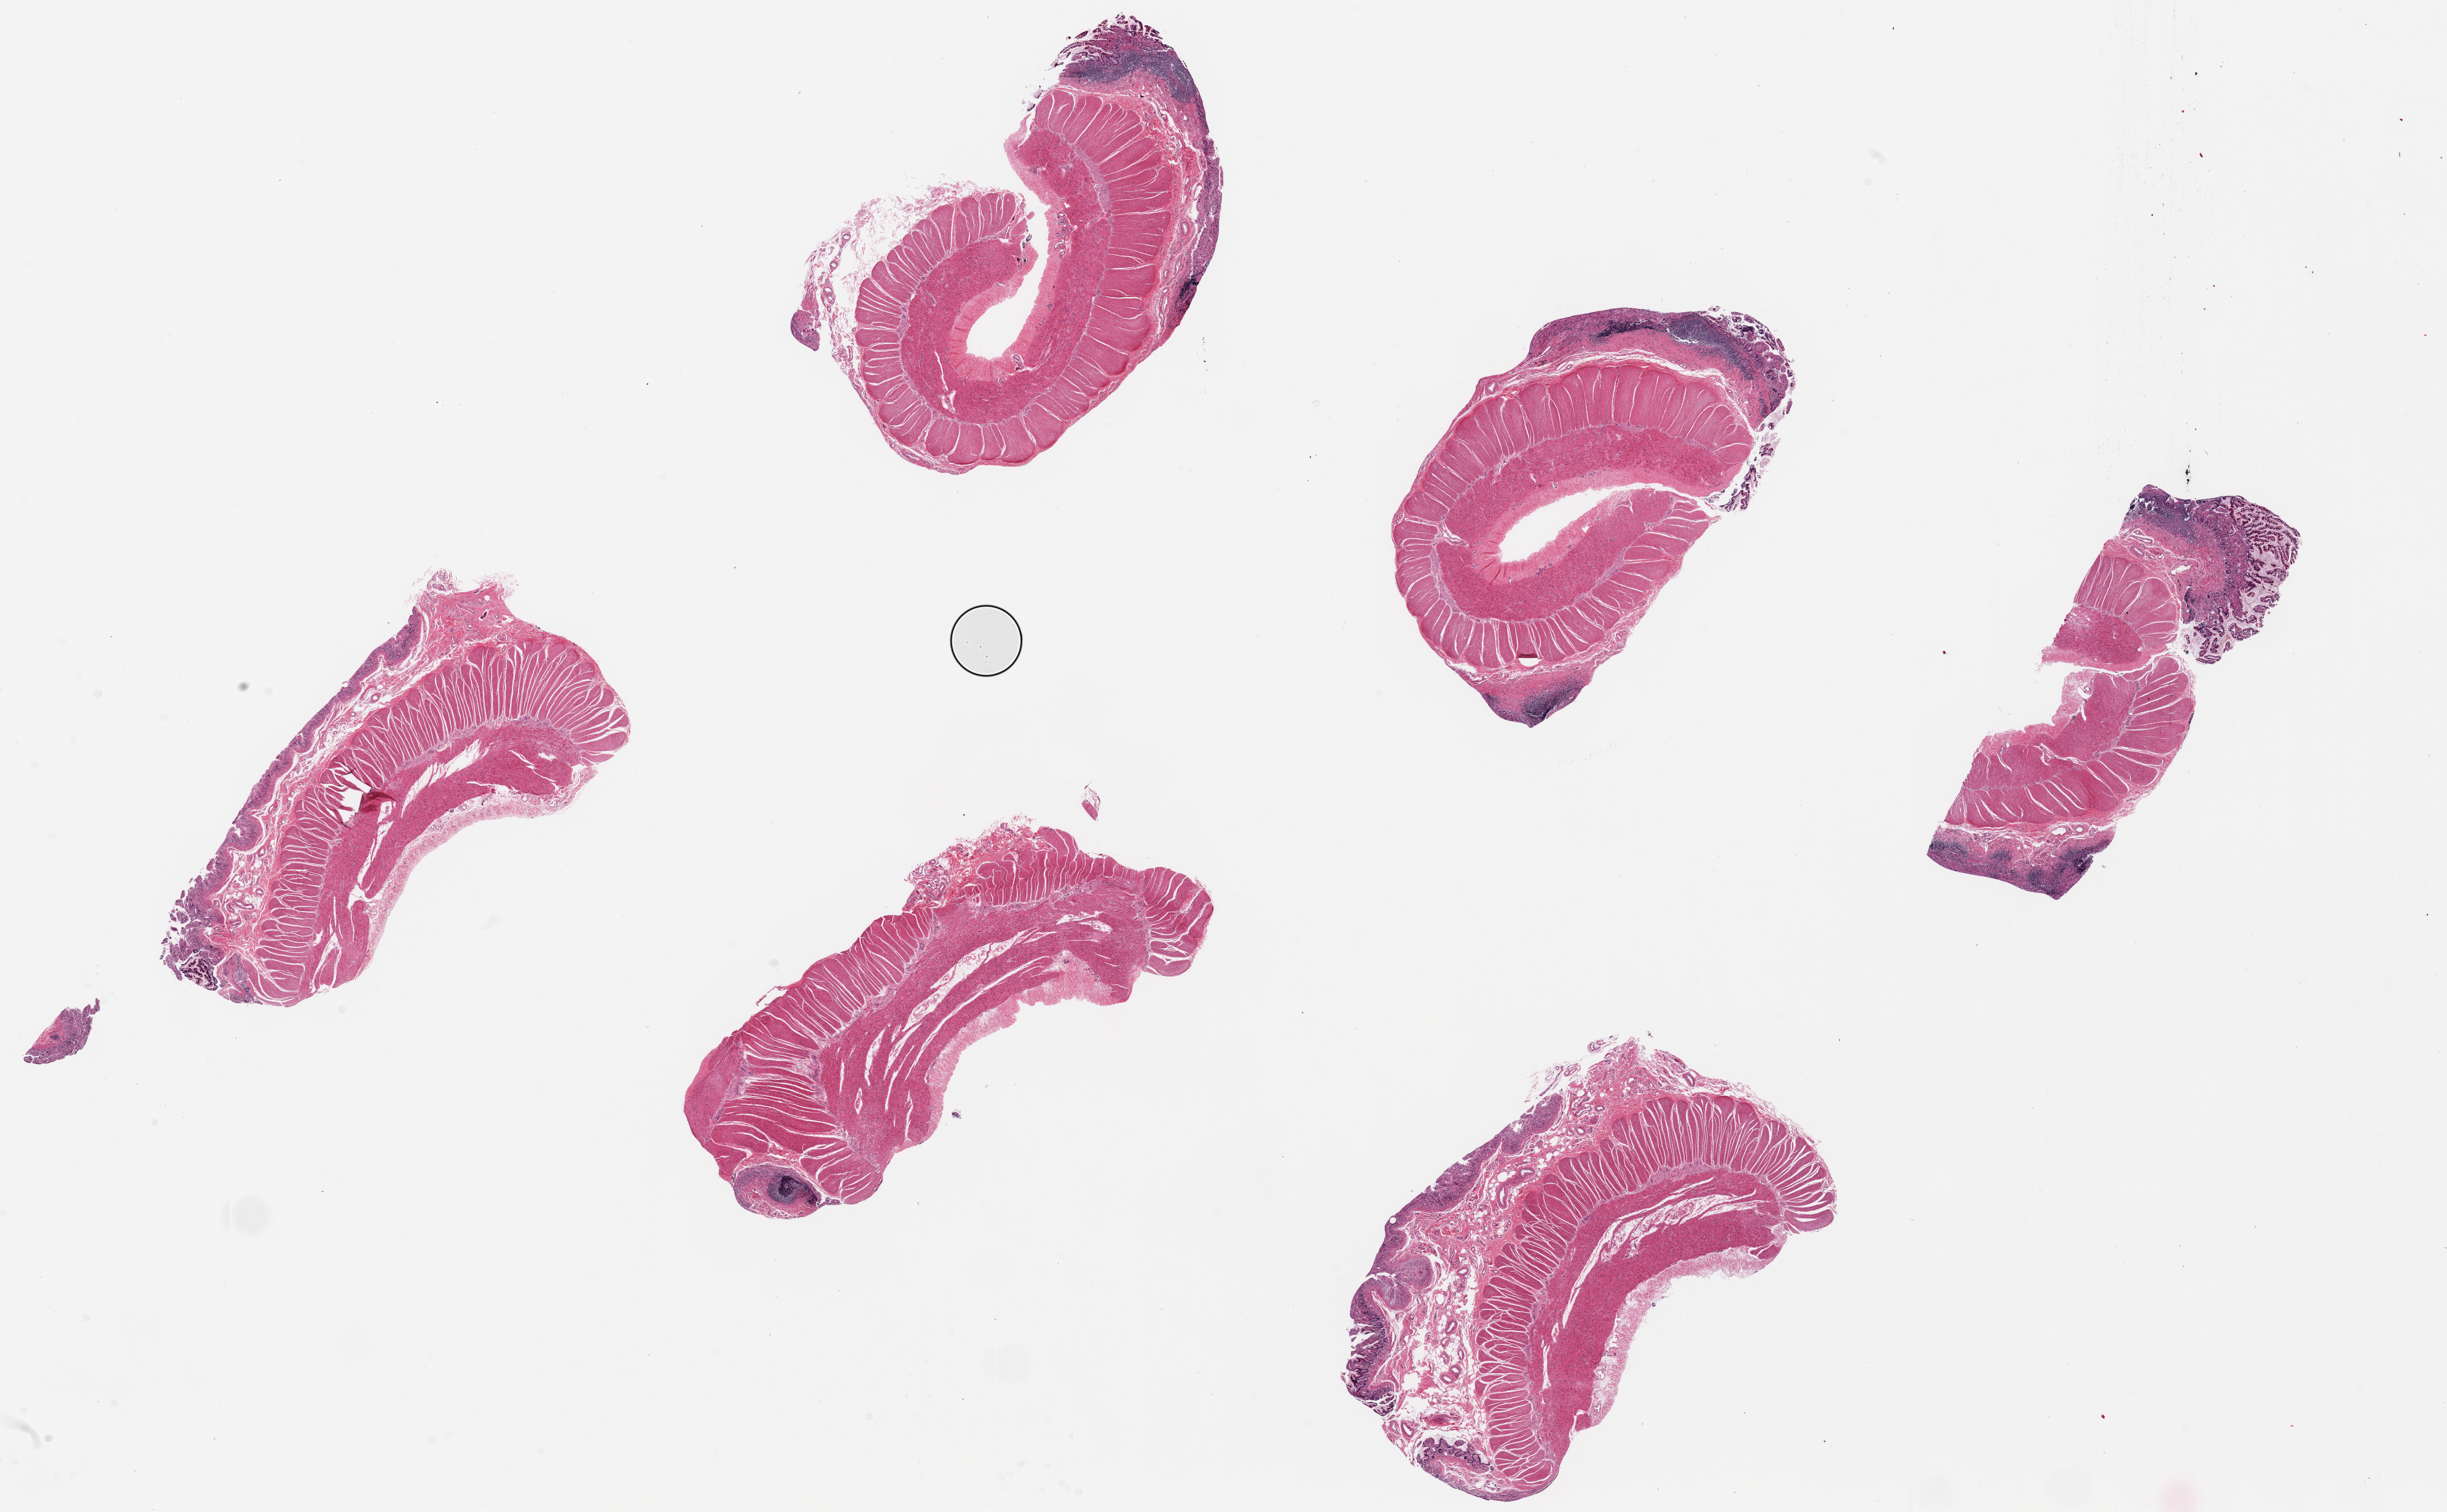
H&E whole-slide image — shown as a low-resolution overview of the whole scanned area (about 31.5 x 19.5 mm, acquisition: 20x scan). PAXgene-fixed, paraffin-embedded tissue. Sampled site (target tissue): transverse colon. Donor tissue sample. Female donor.
- pathologist's review note for this sample: 6 pieces, up to 7x3mm; ~10% mucosa, sloughing